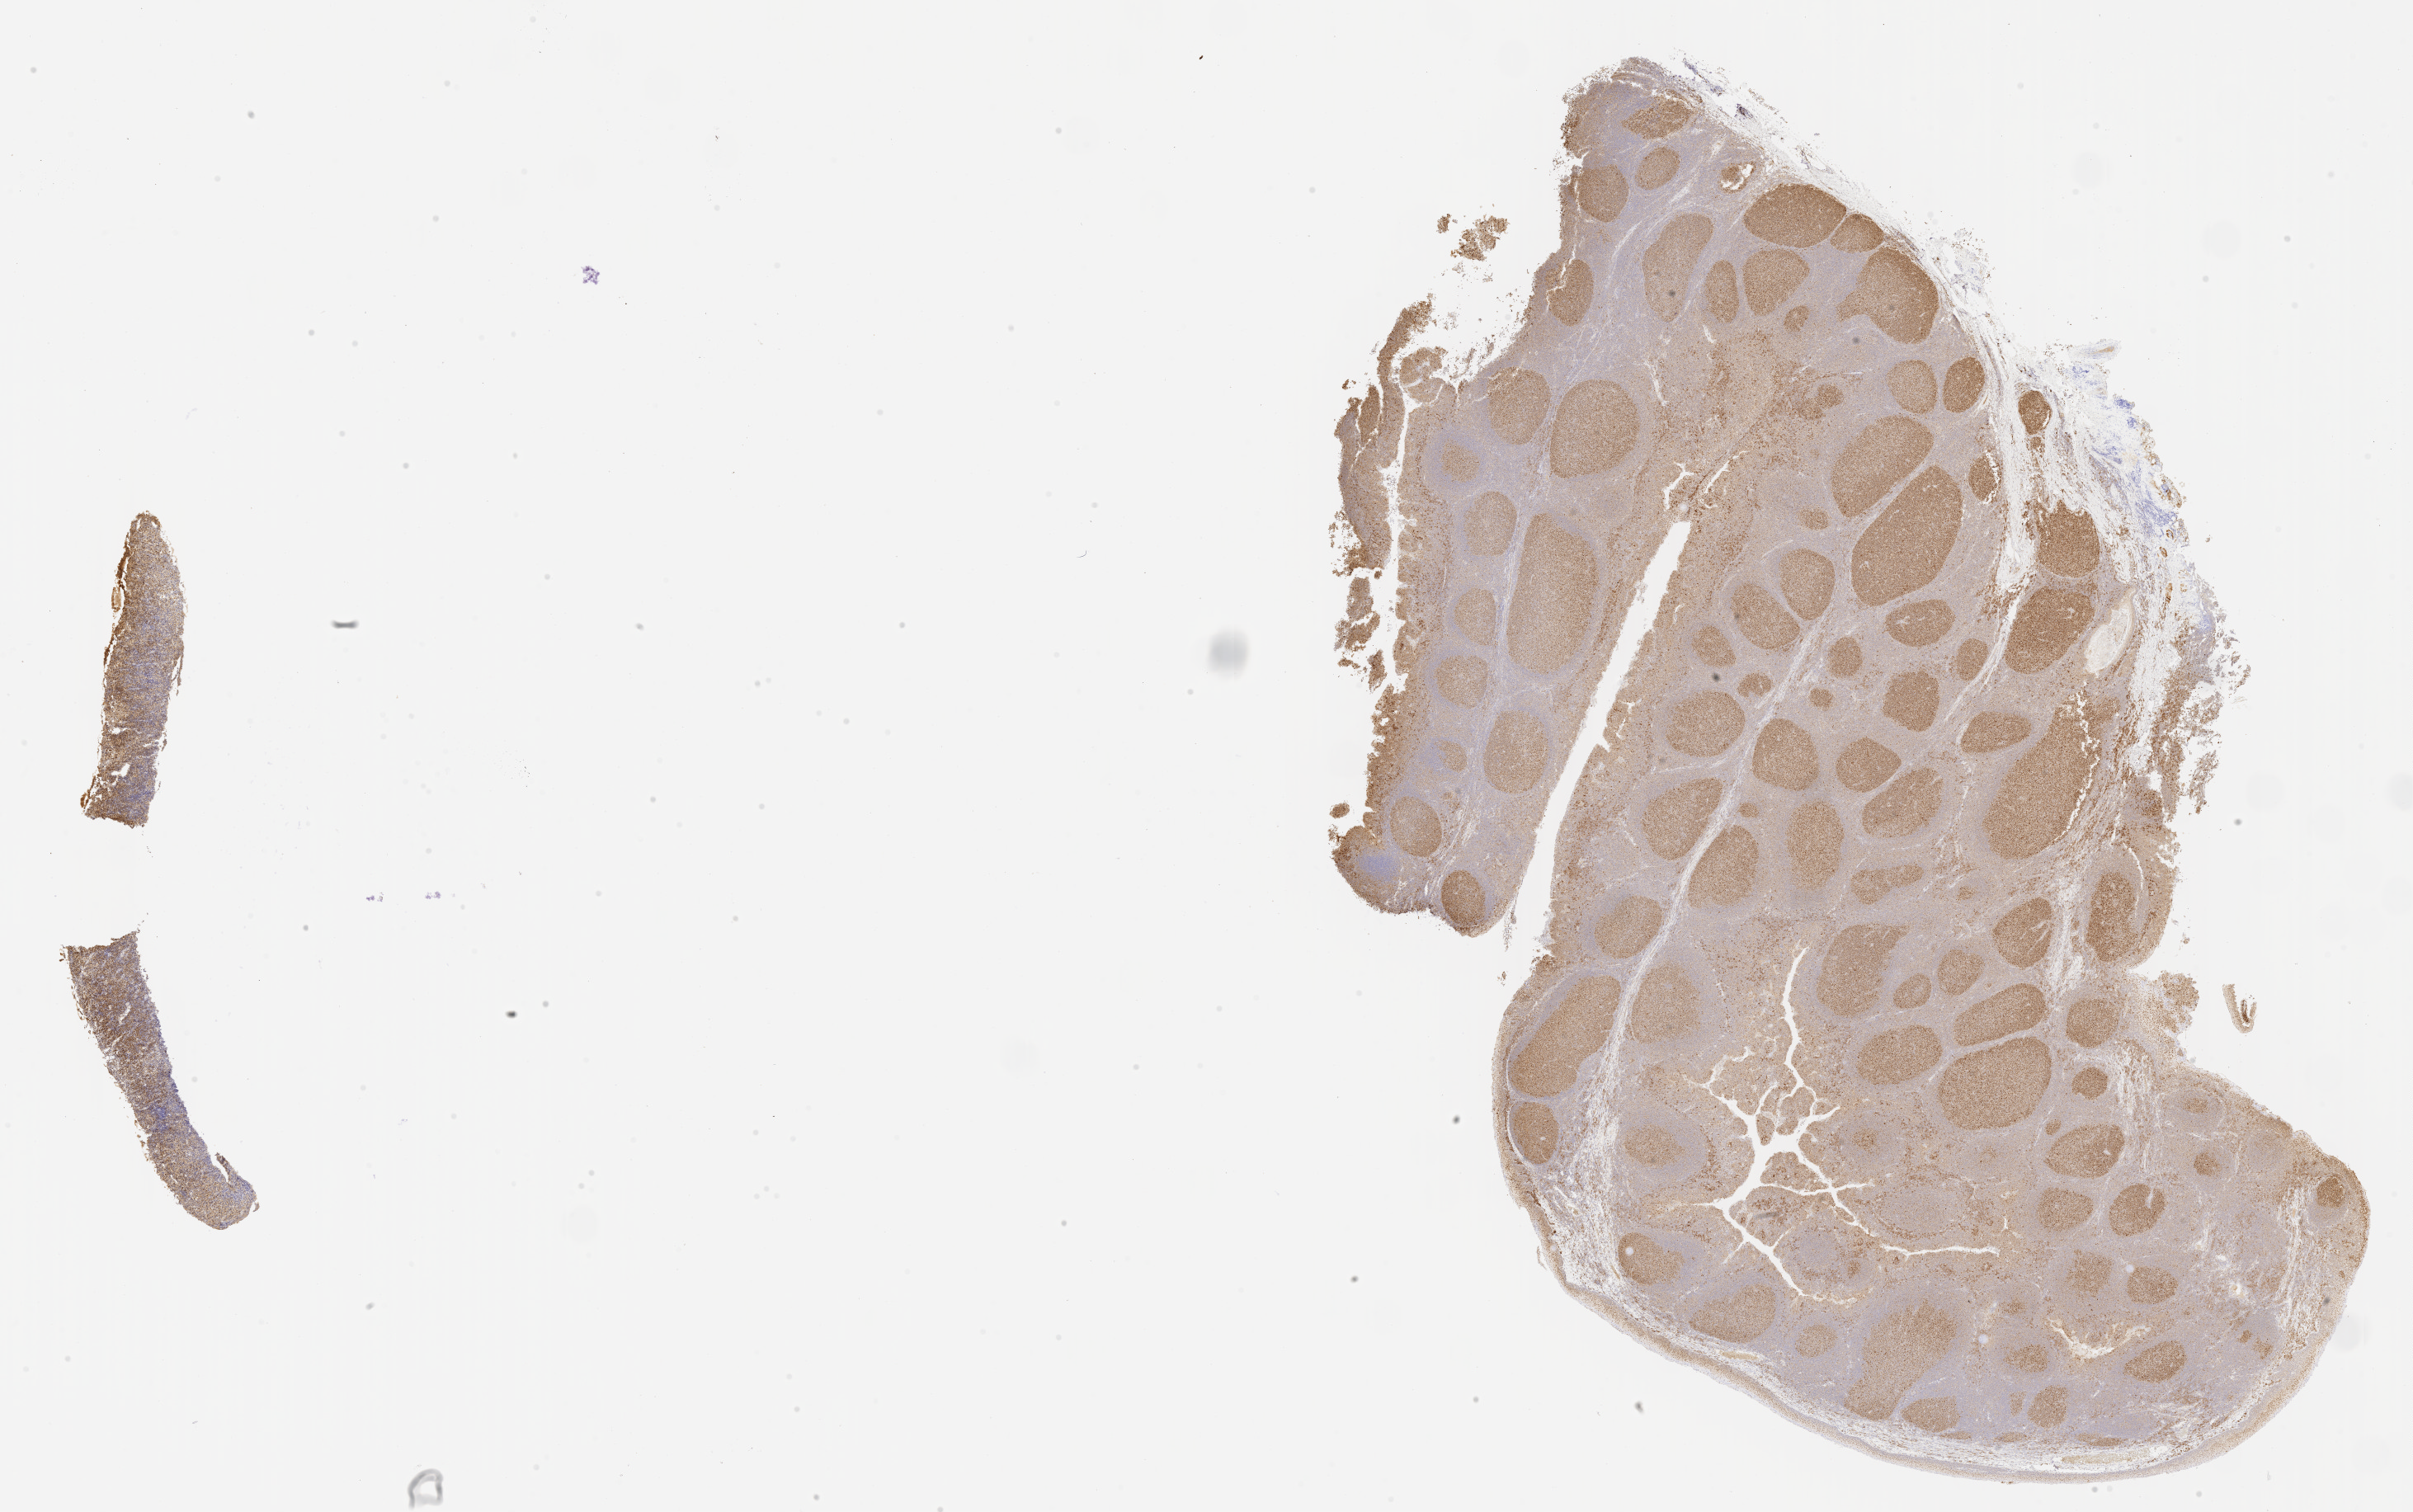
IHC for BCL6, whole-slide image, a low-resolution overview of the entire scanned area, about 23.6 x 14.8 mm. Patient sex: male.
Specimen: tumor tissue.